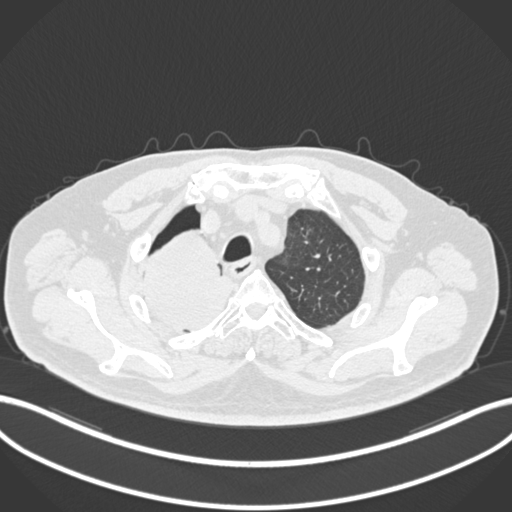
Chest CT, one axial slice. Slice 176 of 218 in the series (ordered by position). 120 kVp. Lung window (W 1500 / L -600 HU). 1 mm slice thickness. 512 × 512 image matrix, field of view 400 × 400 mm. Male patient, age 68 years. Case-level facts recorded for this patient, not image findings: clinical TNM (as recorded): T2a N0 M0.
Structures marked on this image (bounding box drawn by a radiologist):
- lung tumour (recorded histology: adenocarcinoma): bounding box (x1, y1, x2, y2) in pixels: (136, 227, 239, 338)